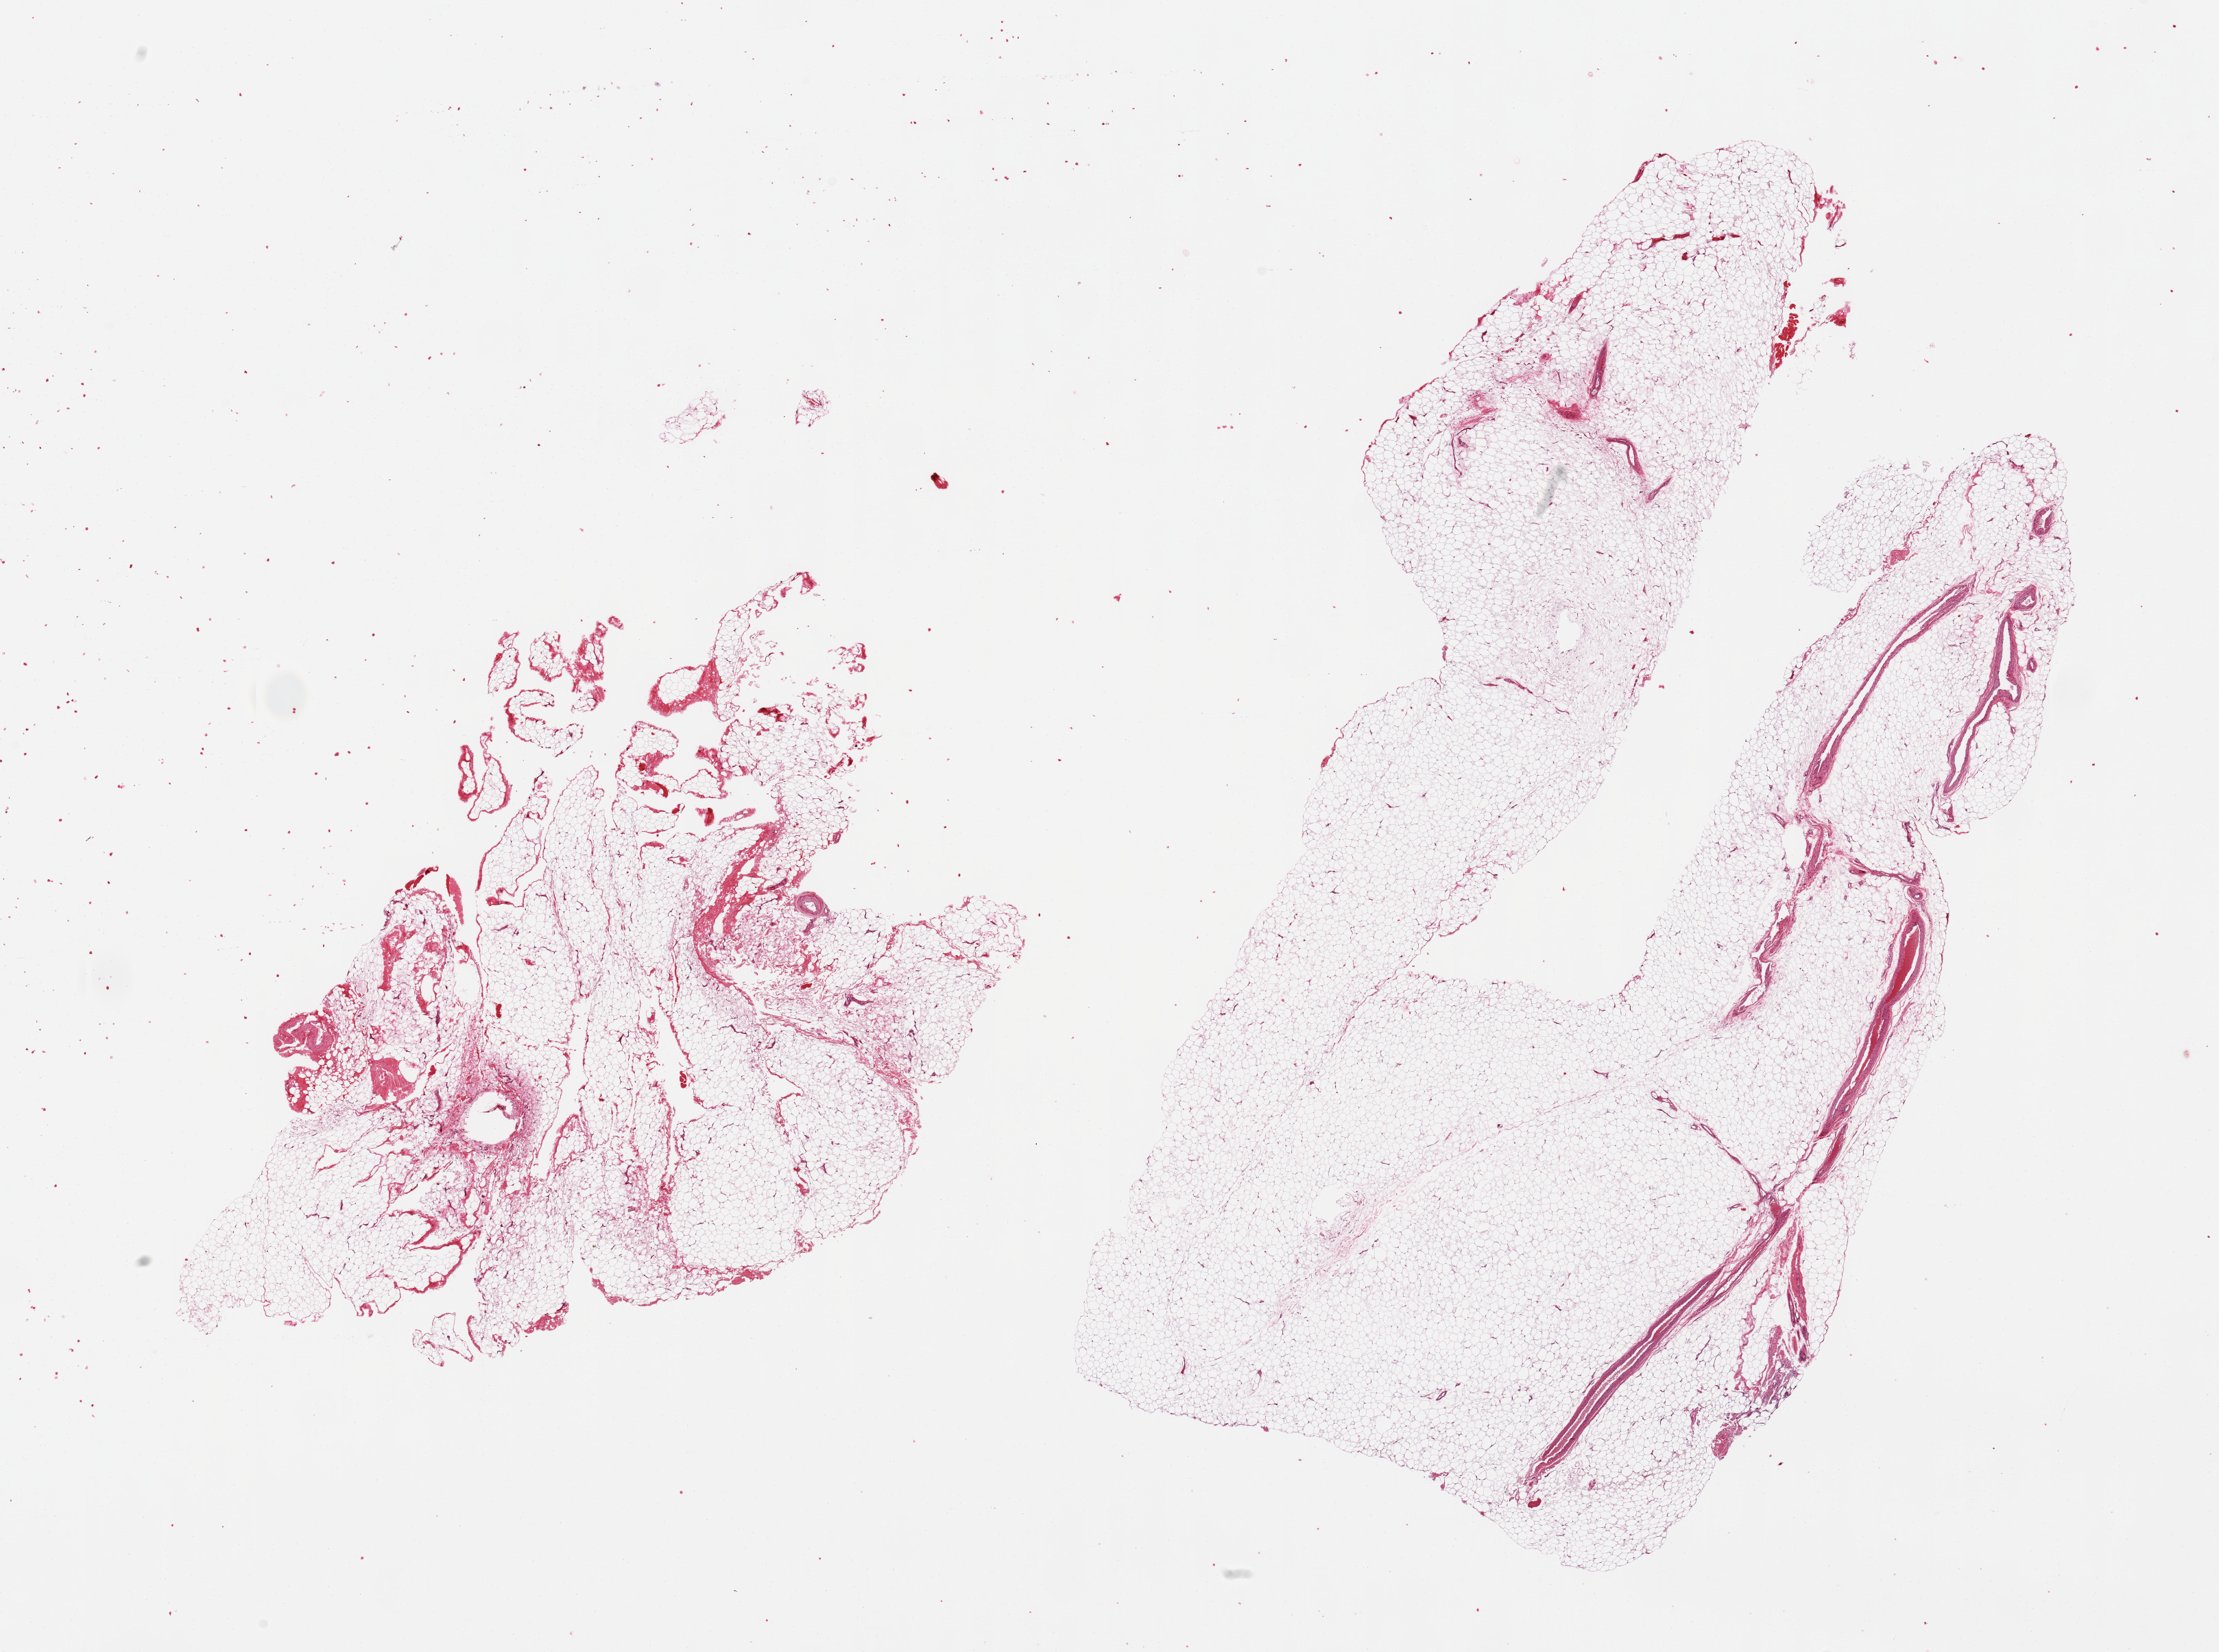
Digitized haematoxylin and eosin-stained section — low-resolution overview of the scanned area, about 25.6 x 19.1 mm (slide scanned at 20x). PAXgene-fixed paraffin-embedded (PFPE) section. Sampled site (target tissue): adipose tissue. Tissue donor sample. Donor: male.
Reviewer comment on this tissue sample: 1 piece; not skin, adipose tissue with small portion of fibrous tissue.